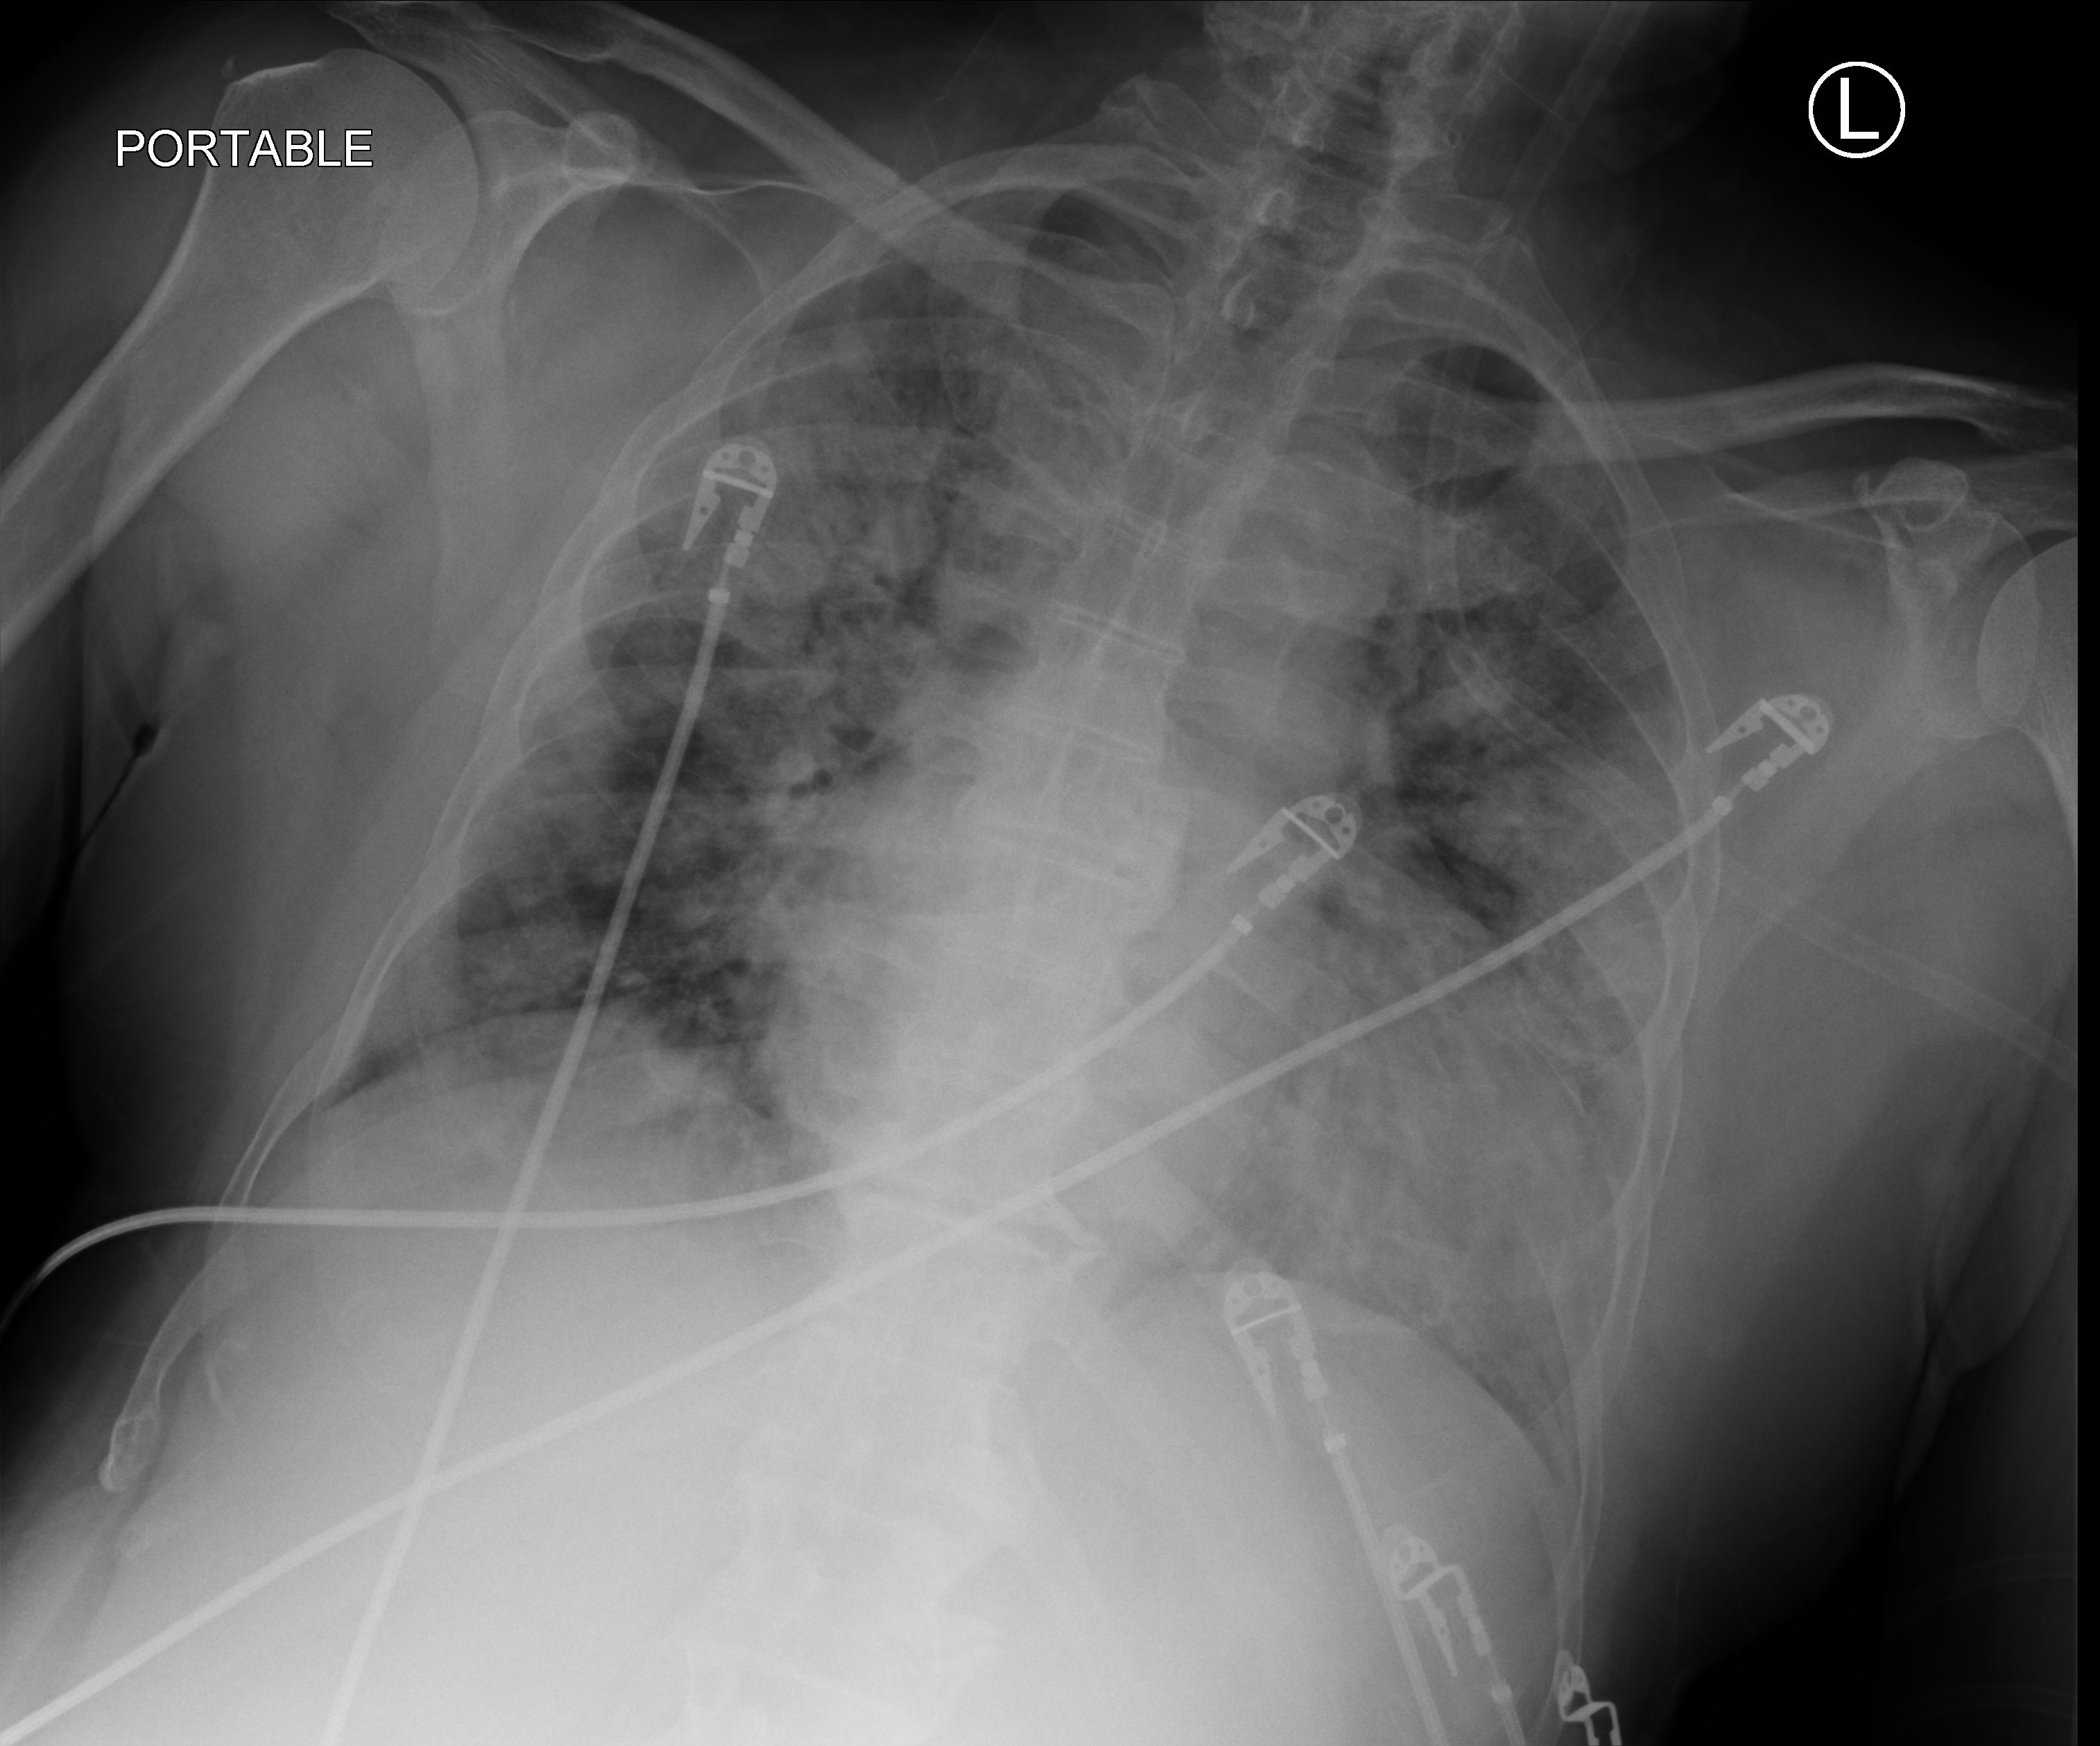
Chest X-ray (portable), anteroposterior (AP) projection. Patient hospitalised with COVID-19; male, aged 60–74 years.
From the hospital-stay record, not from the radiograph (when in the stay this image was taken is not recorded): admitted to intensive care during this hospital stay: yes; chronic kidney disease (admission record): no.